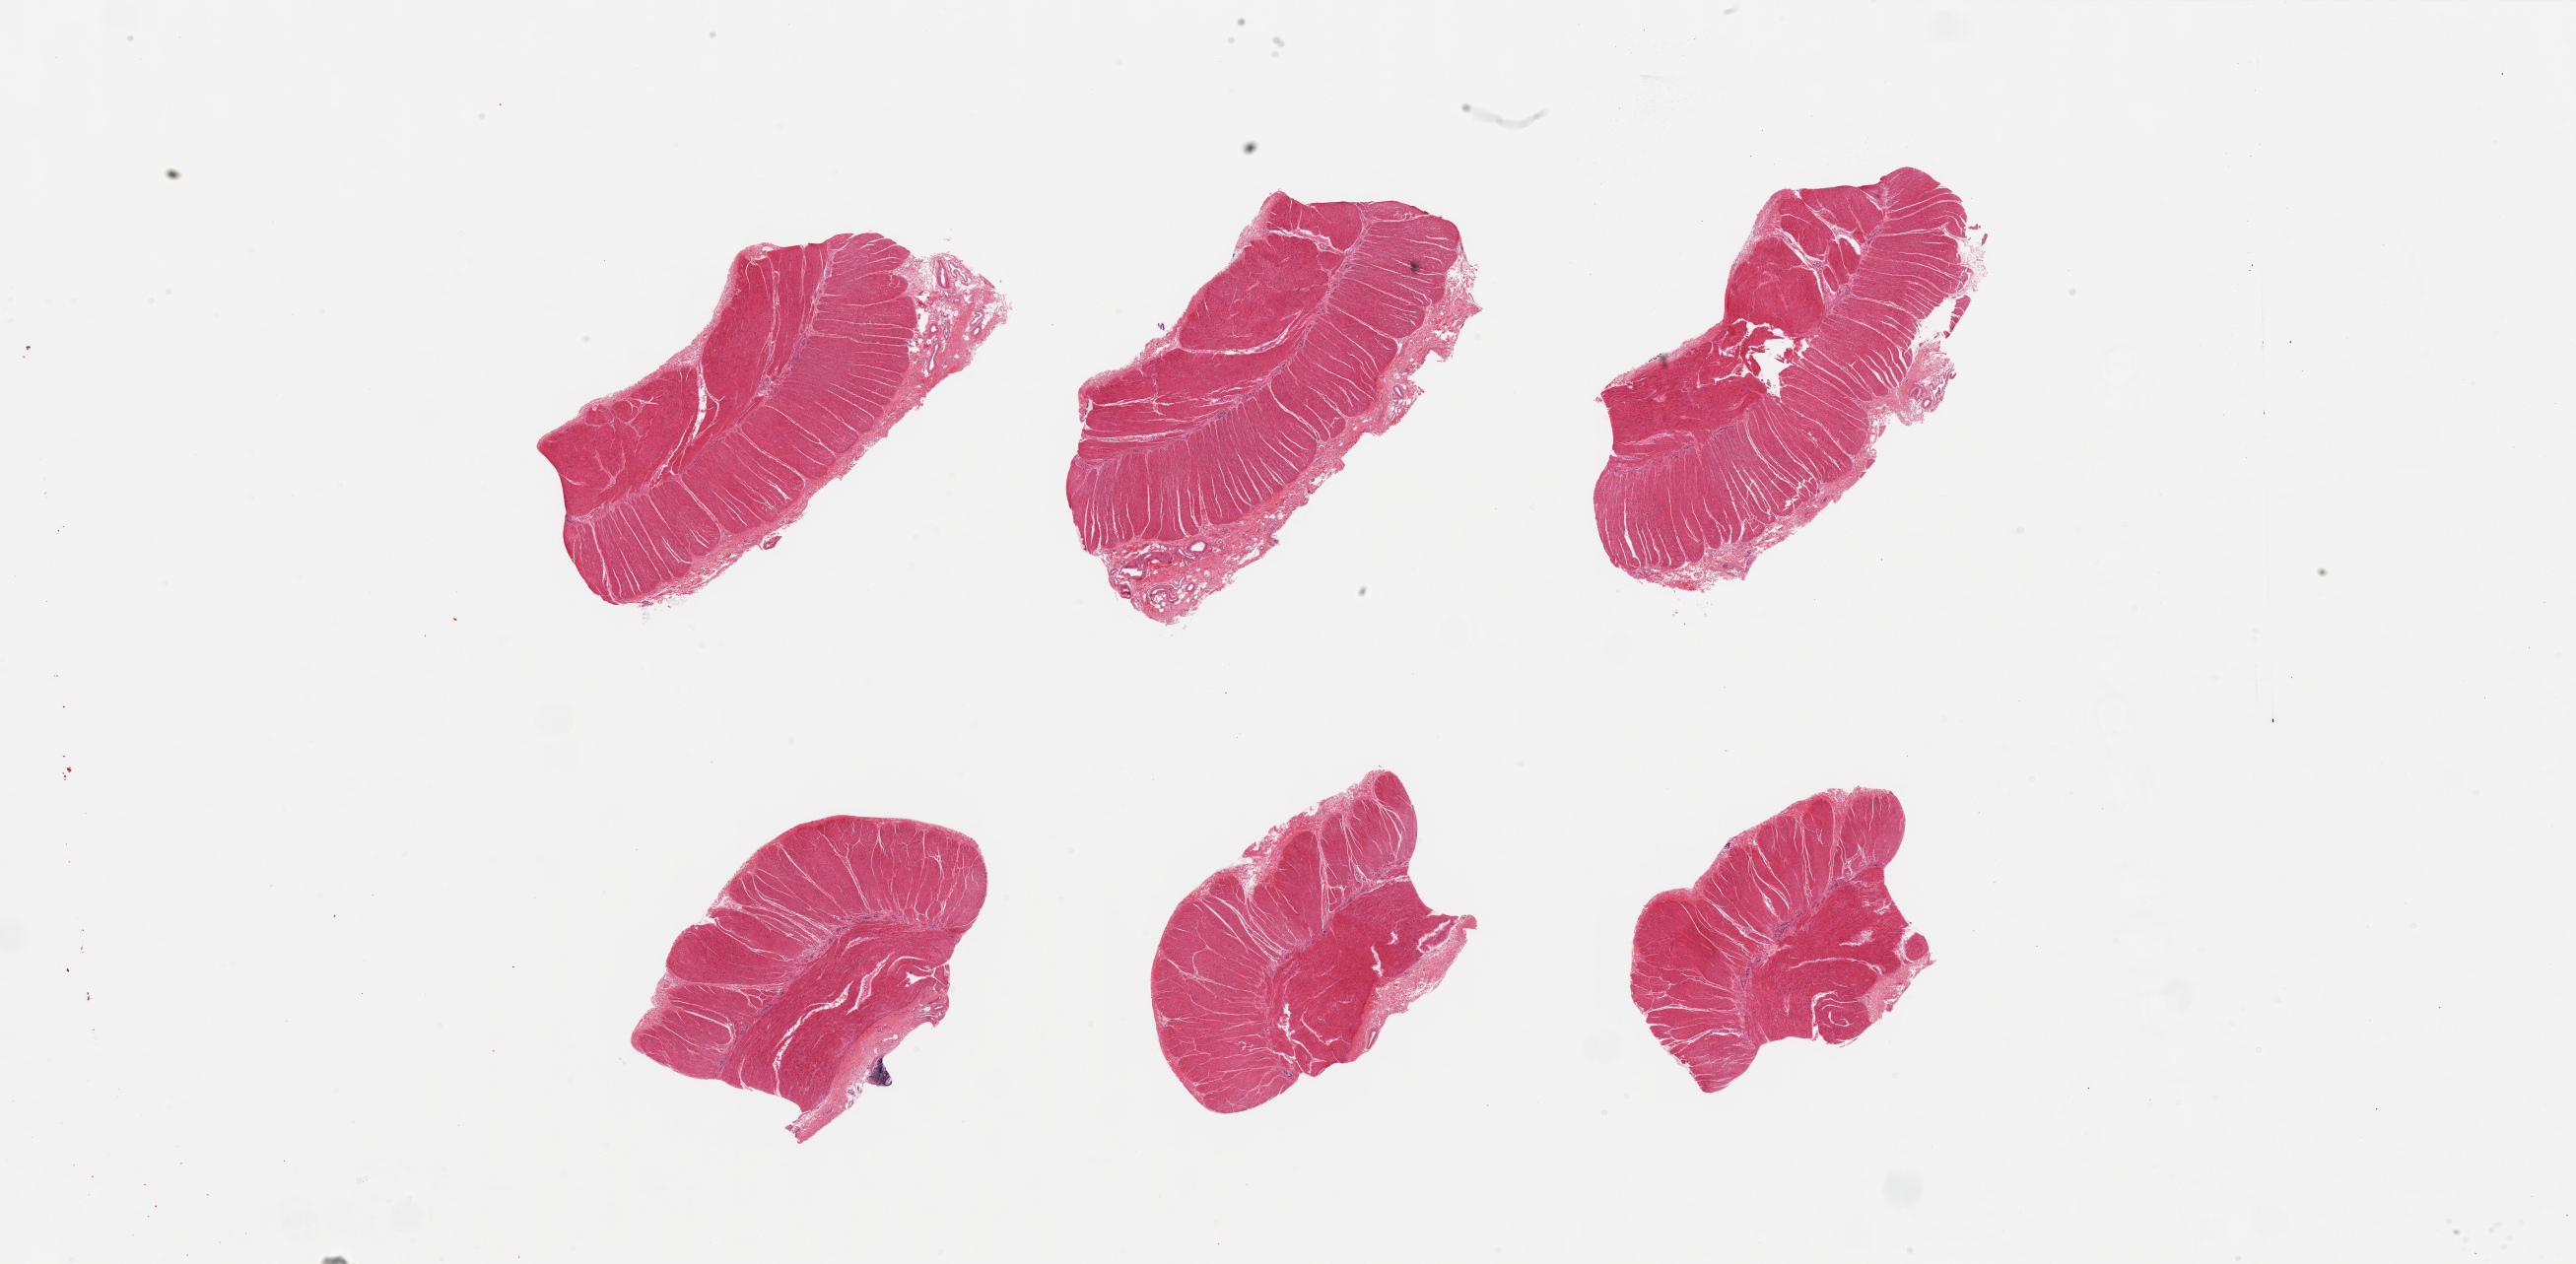
Digitized hematoxylin and eosin (H&E)-stained section, low-resolution overview of the scanned area, about 41.3 x 20.3 mm, PAXgene-fixed, paraffin-embedded tissue, target tissue: sigmoid colon, tissue donor sample.
Pathologist's review note for this sample: 6 pieces; well dissected muscularis (target).